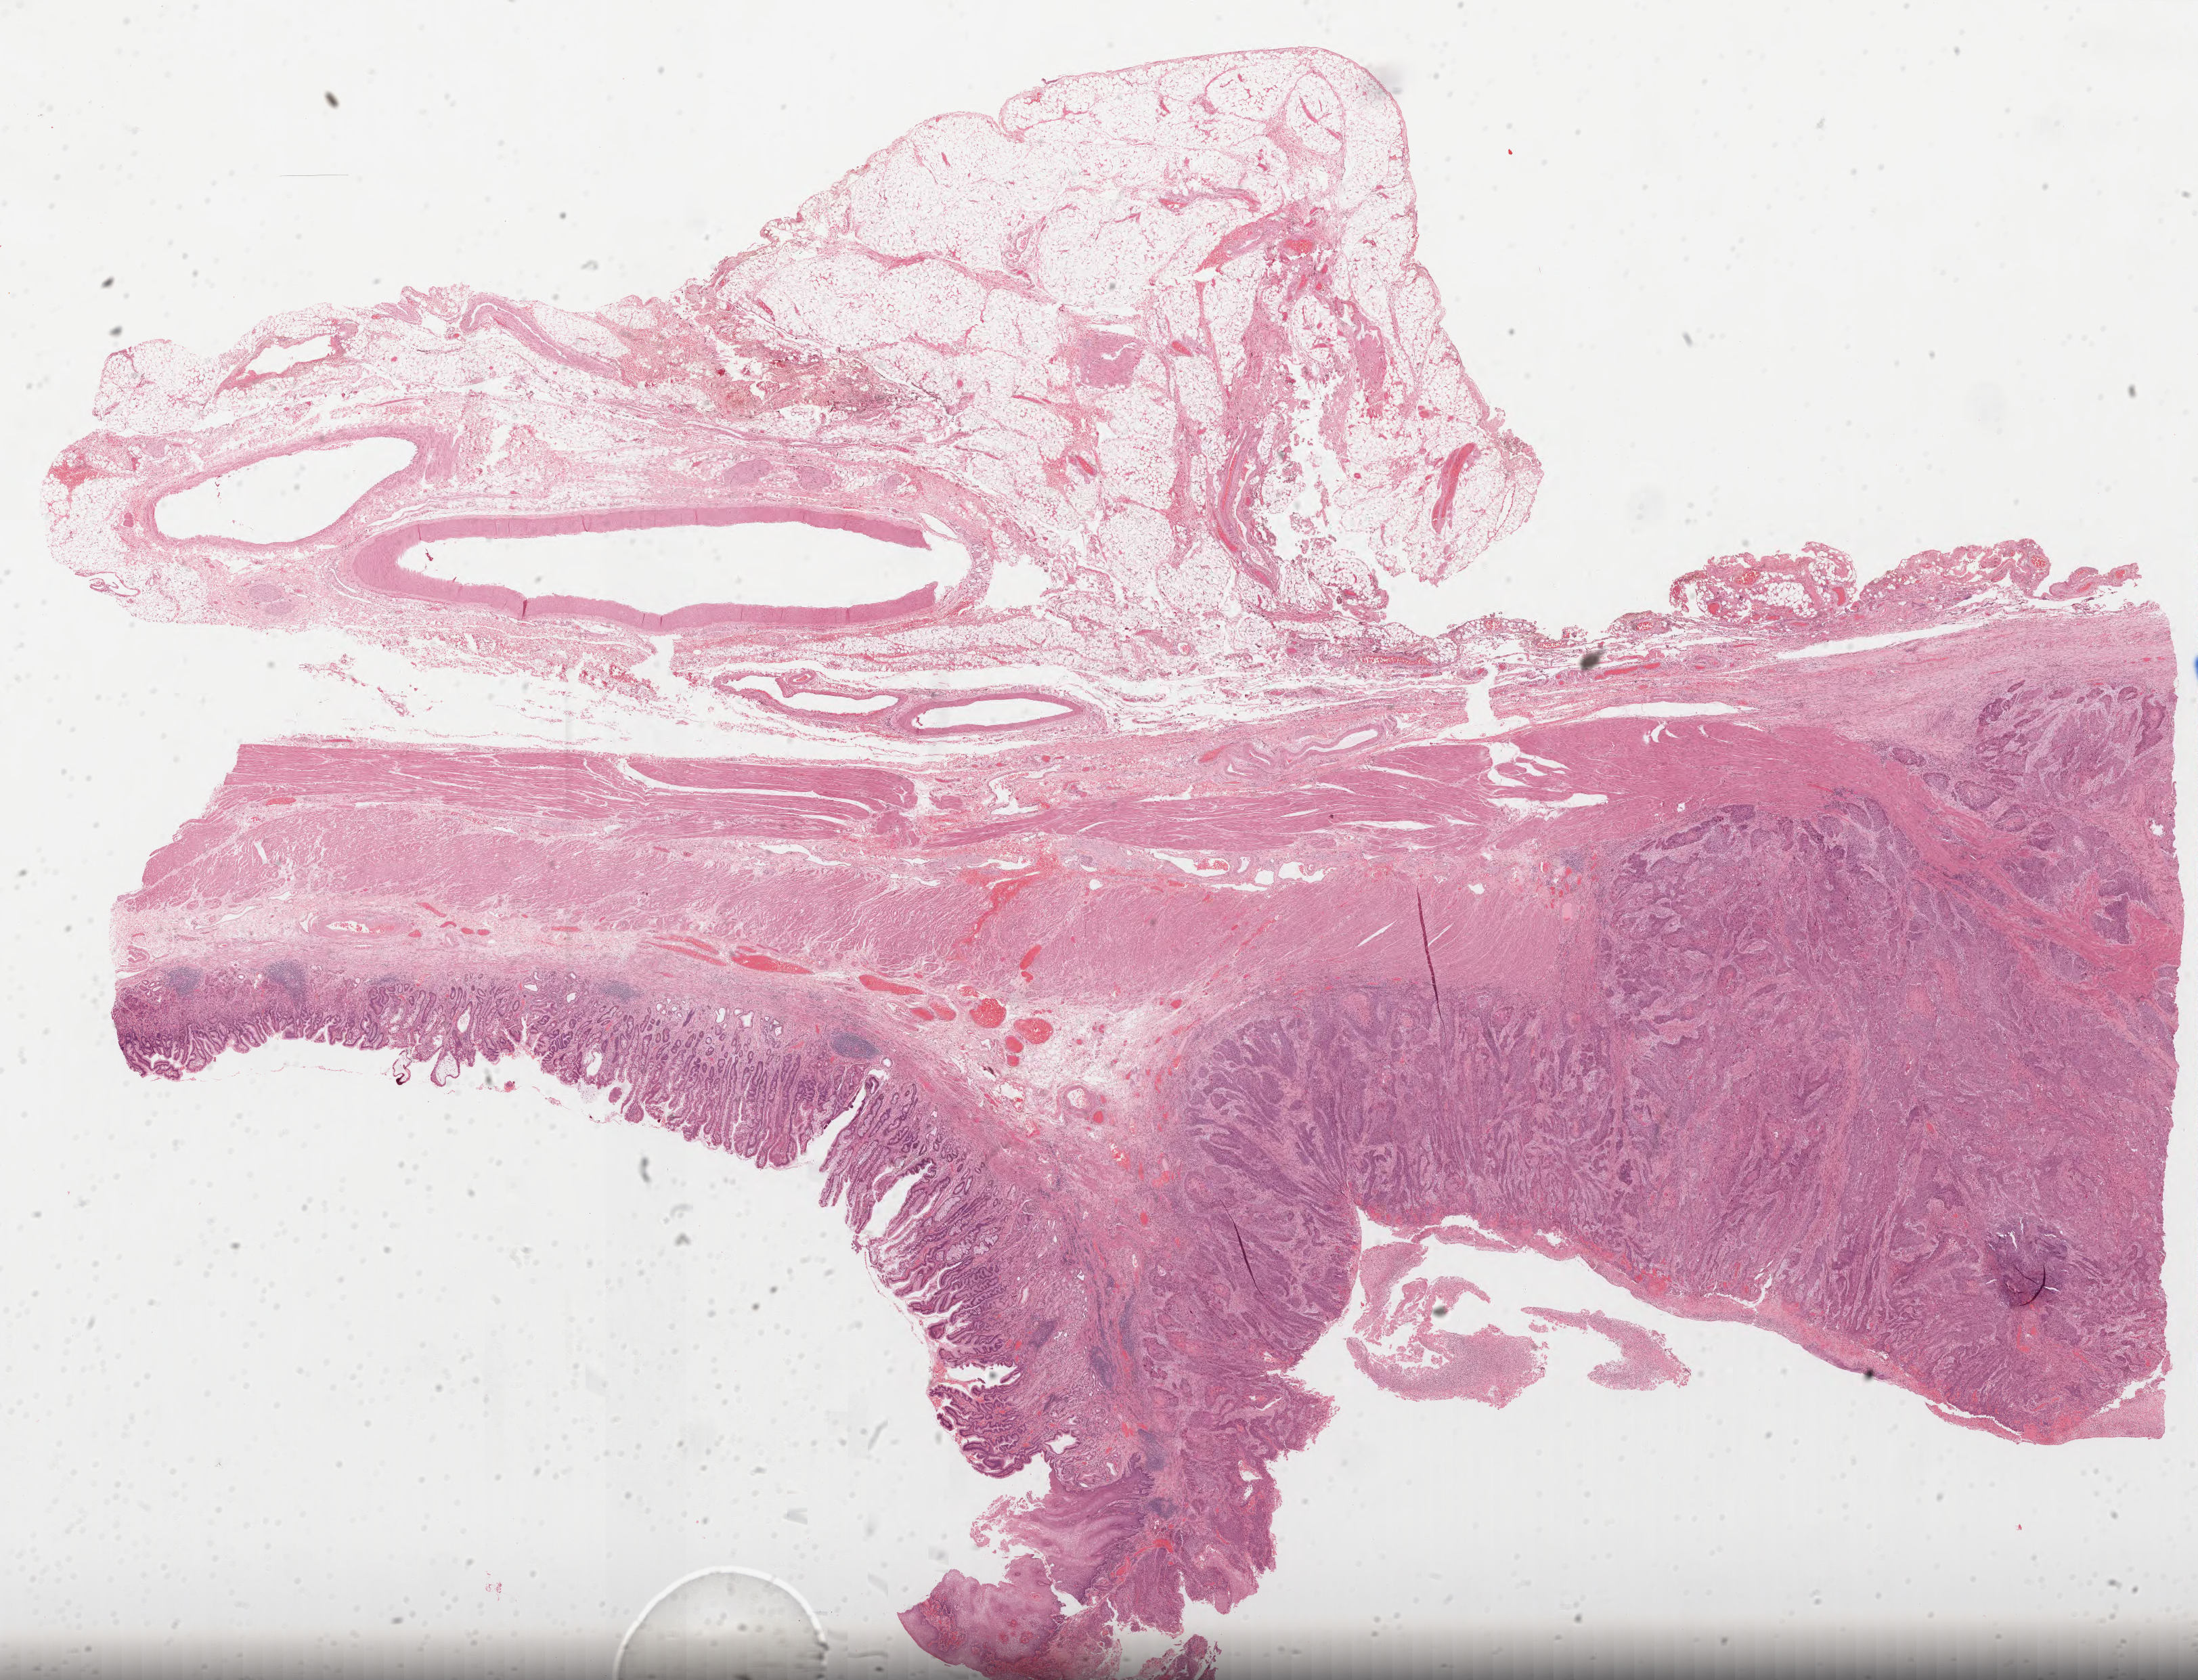
Whole-slide histology image, Hematoxylin and eosin (H&E) stained, shown as a low-resolution overview of the whole scanned area (about 26.2 x 20.0 mm, acquisition: 40x scan). Formalin-fixed paraffin-embedded (FFPE) diagnostic section. Sample: primary tumour, esophagus. Patient: male, age at initial diagnosis 51 years. Histologic grade: G2 (moderately differentiated).
- lymph nodes positive (case pathology): 4 of 19 examined
- diagnosis: Squamous cell carcinoma, NOS (lower third of esophagus)
- AJCC pathologic stage: IIB (6th edition)